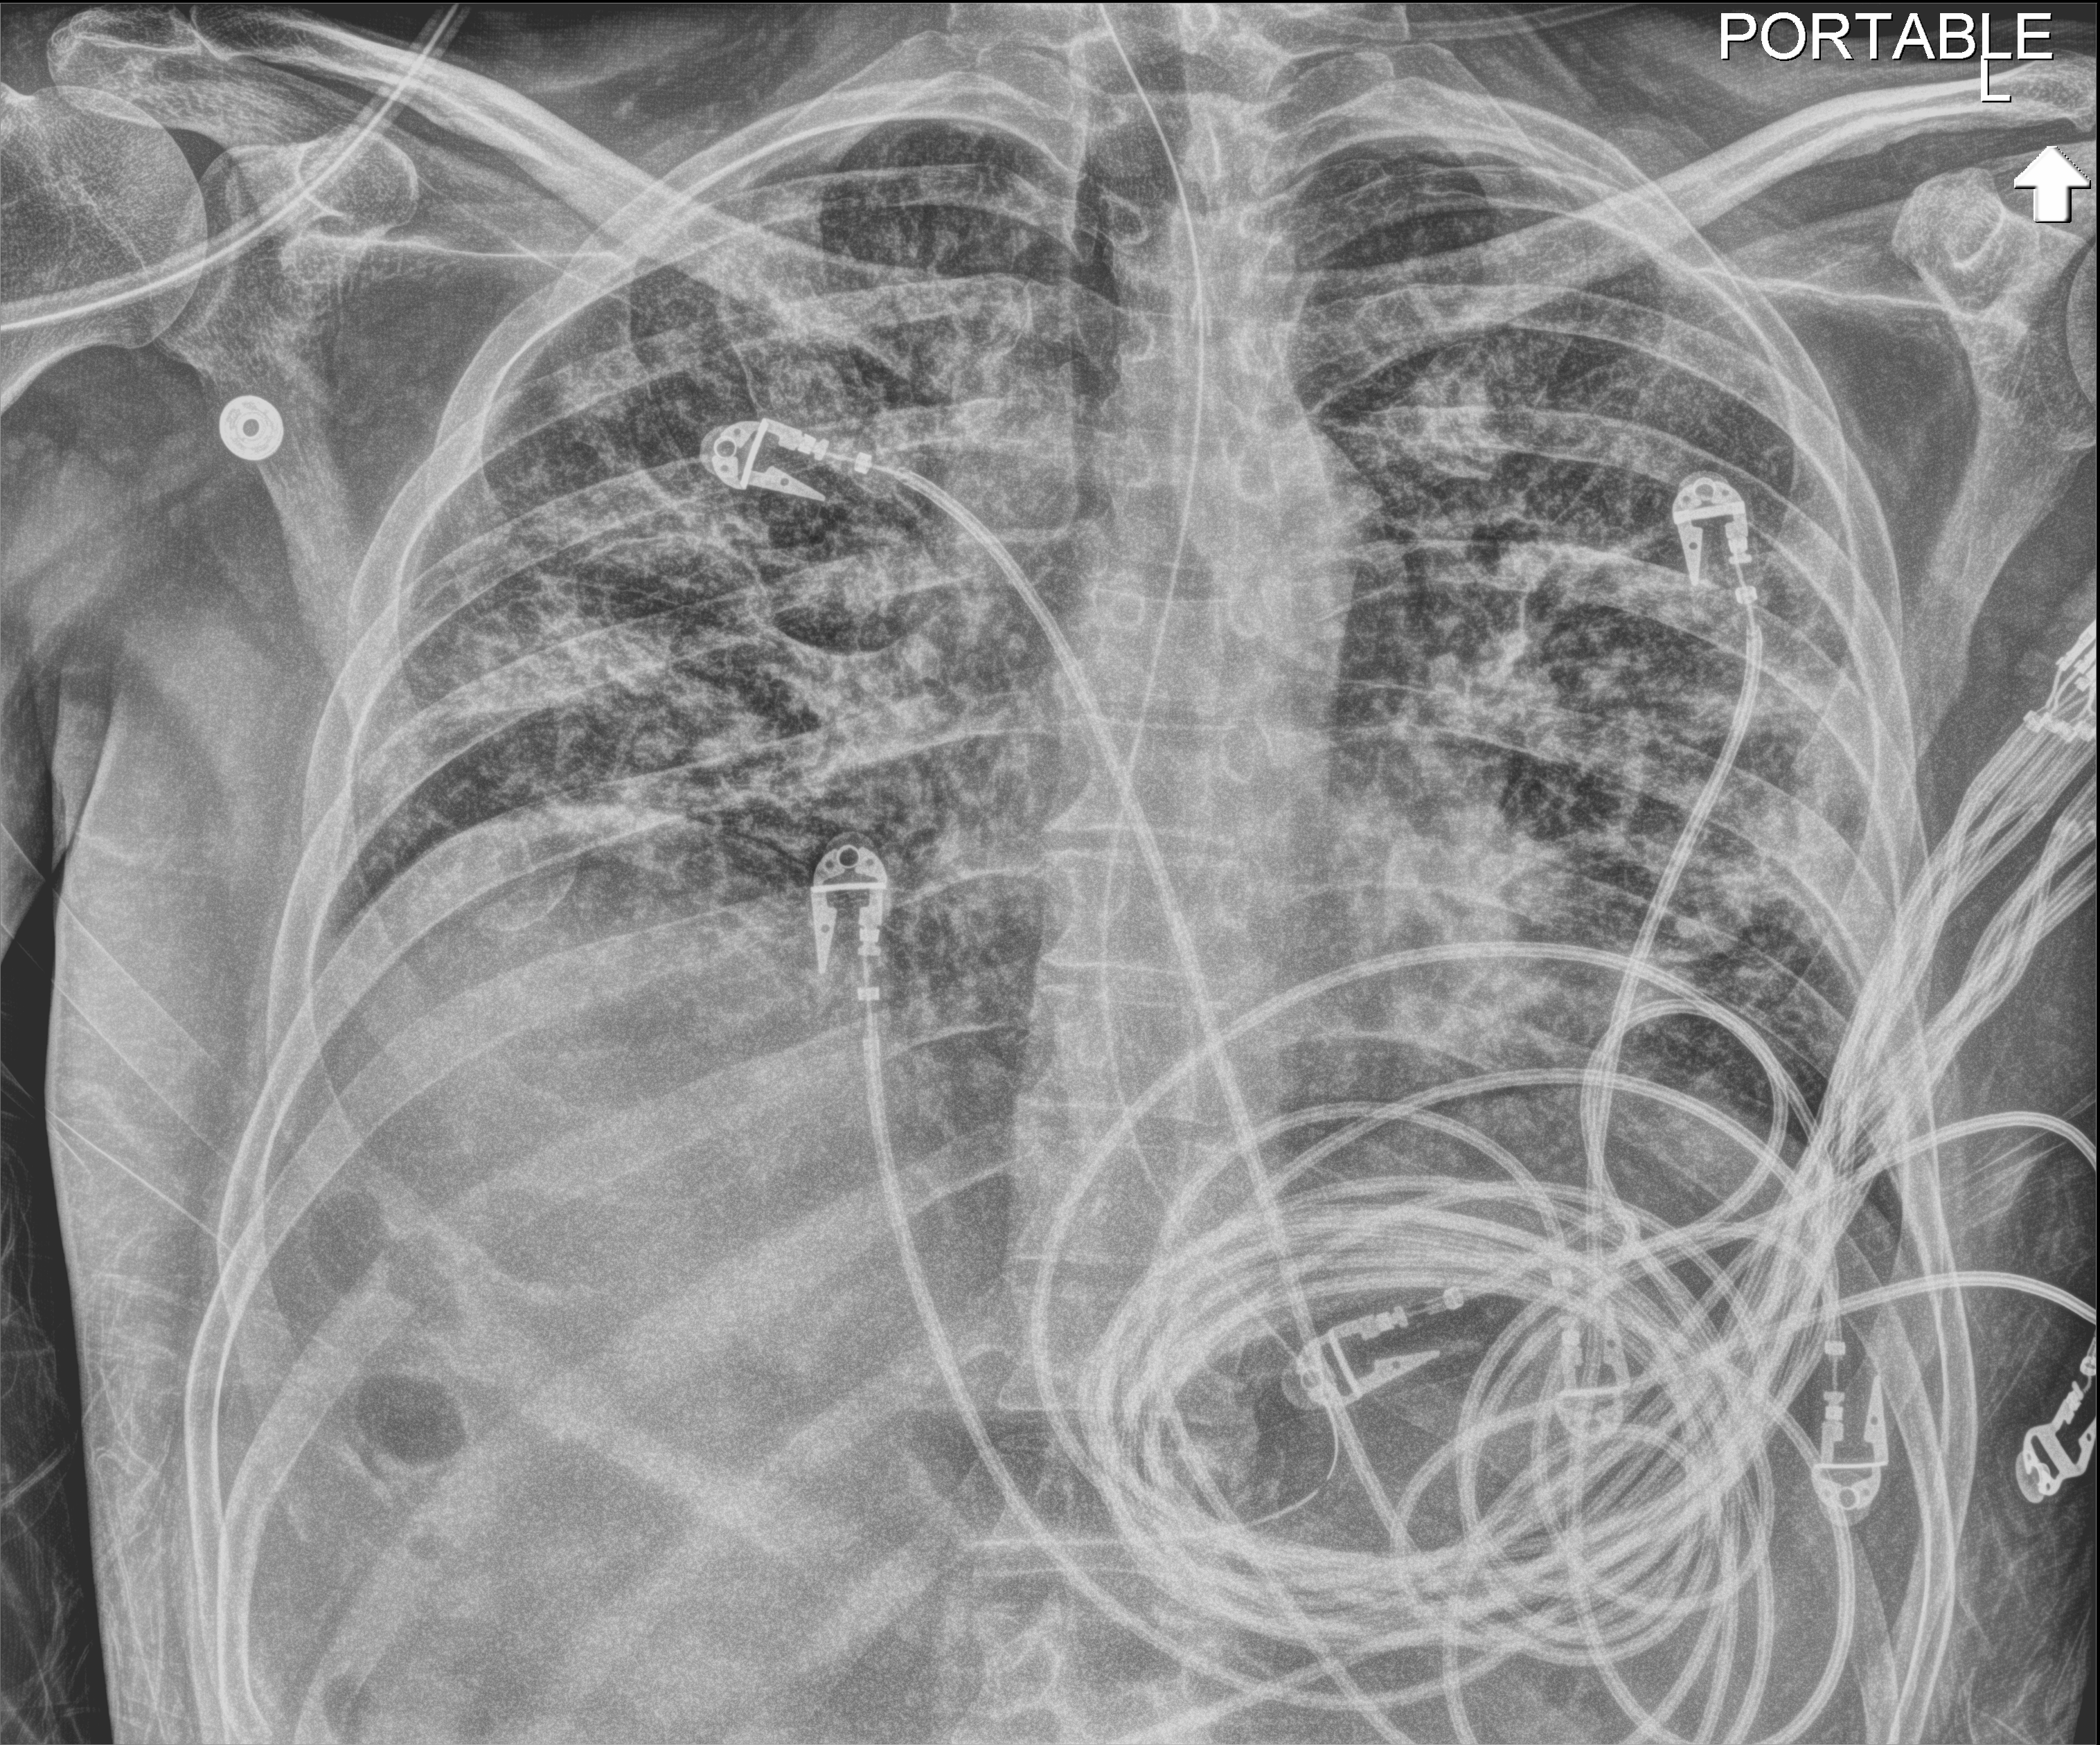
Portable chest radiograph, anteroposterior (AP) projection. Male patient hospitalised with COVID-19, age 18–59 years.
Admission-level facts for this patient (not findings on this image; timing relative to this image not recorded): admitted to intensive care during this hospital stay: yes; length of hospital stay: 48 days; diabetes (admission record): no.